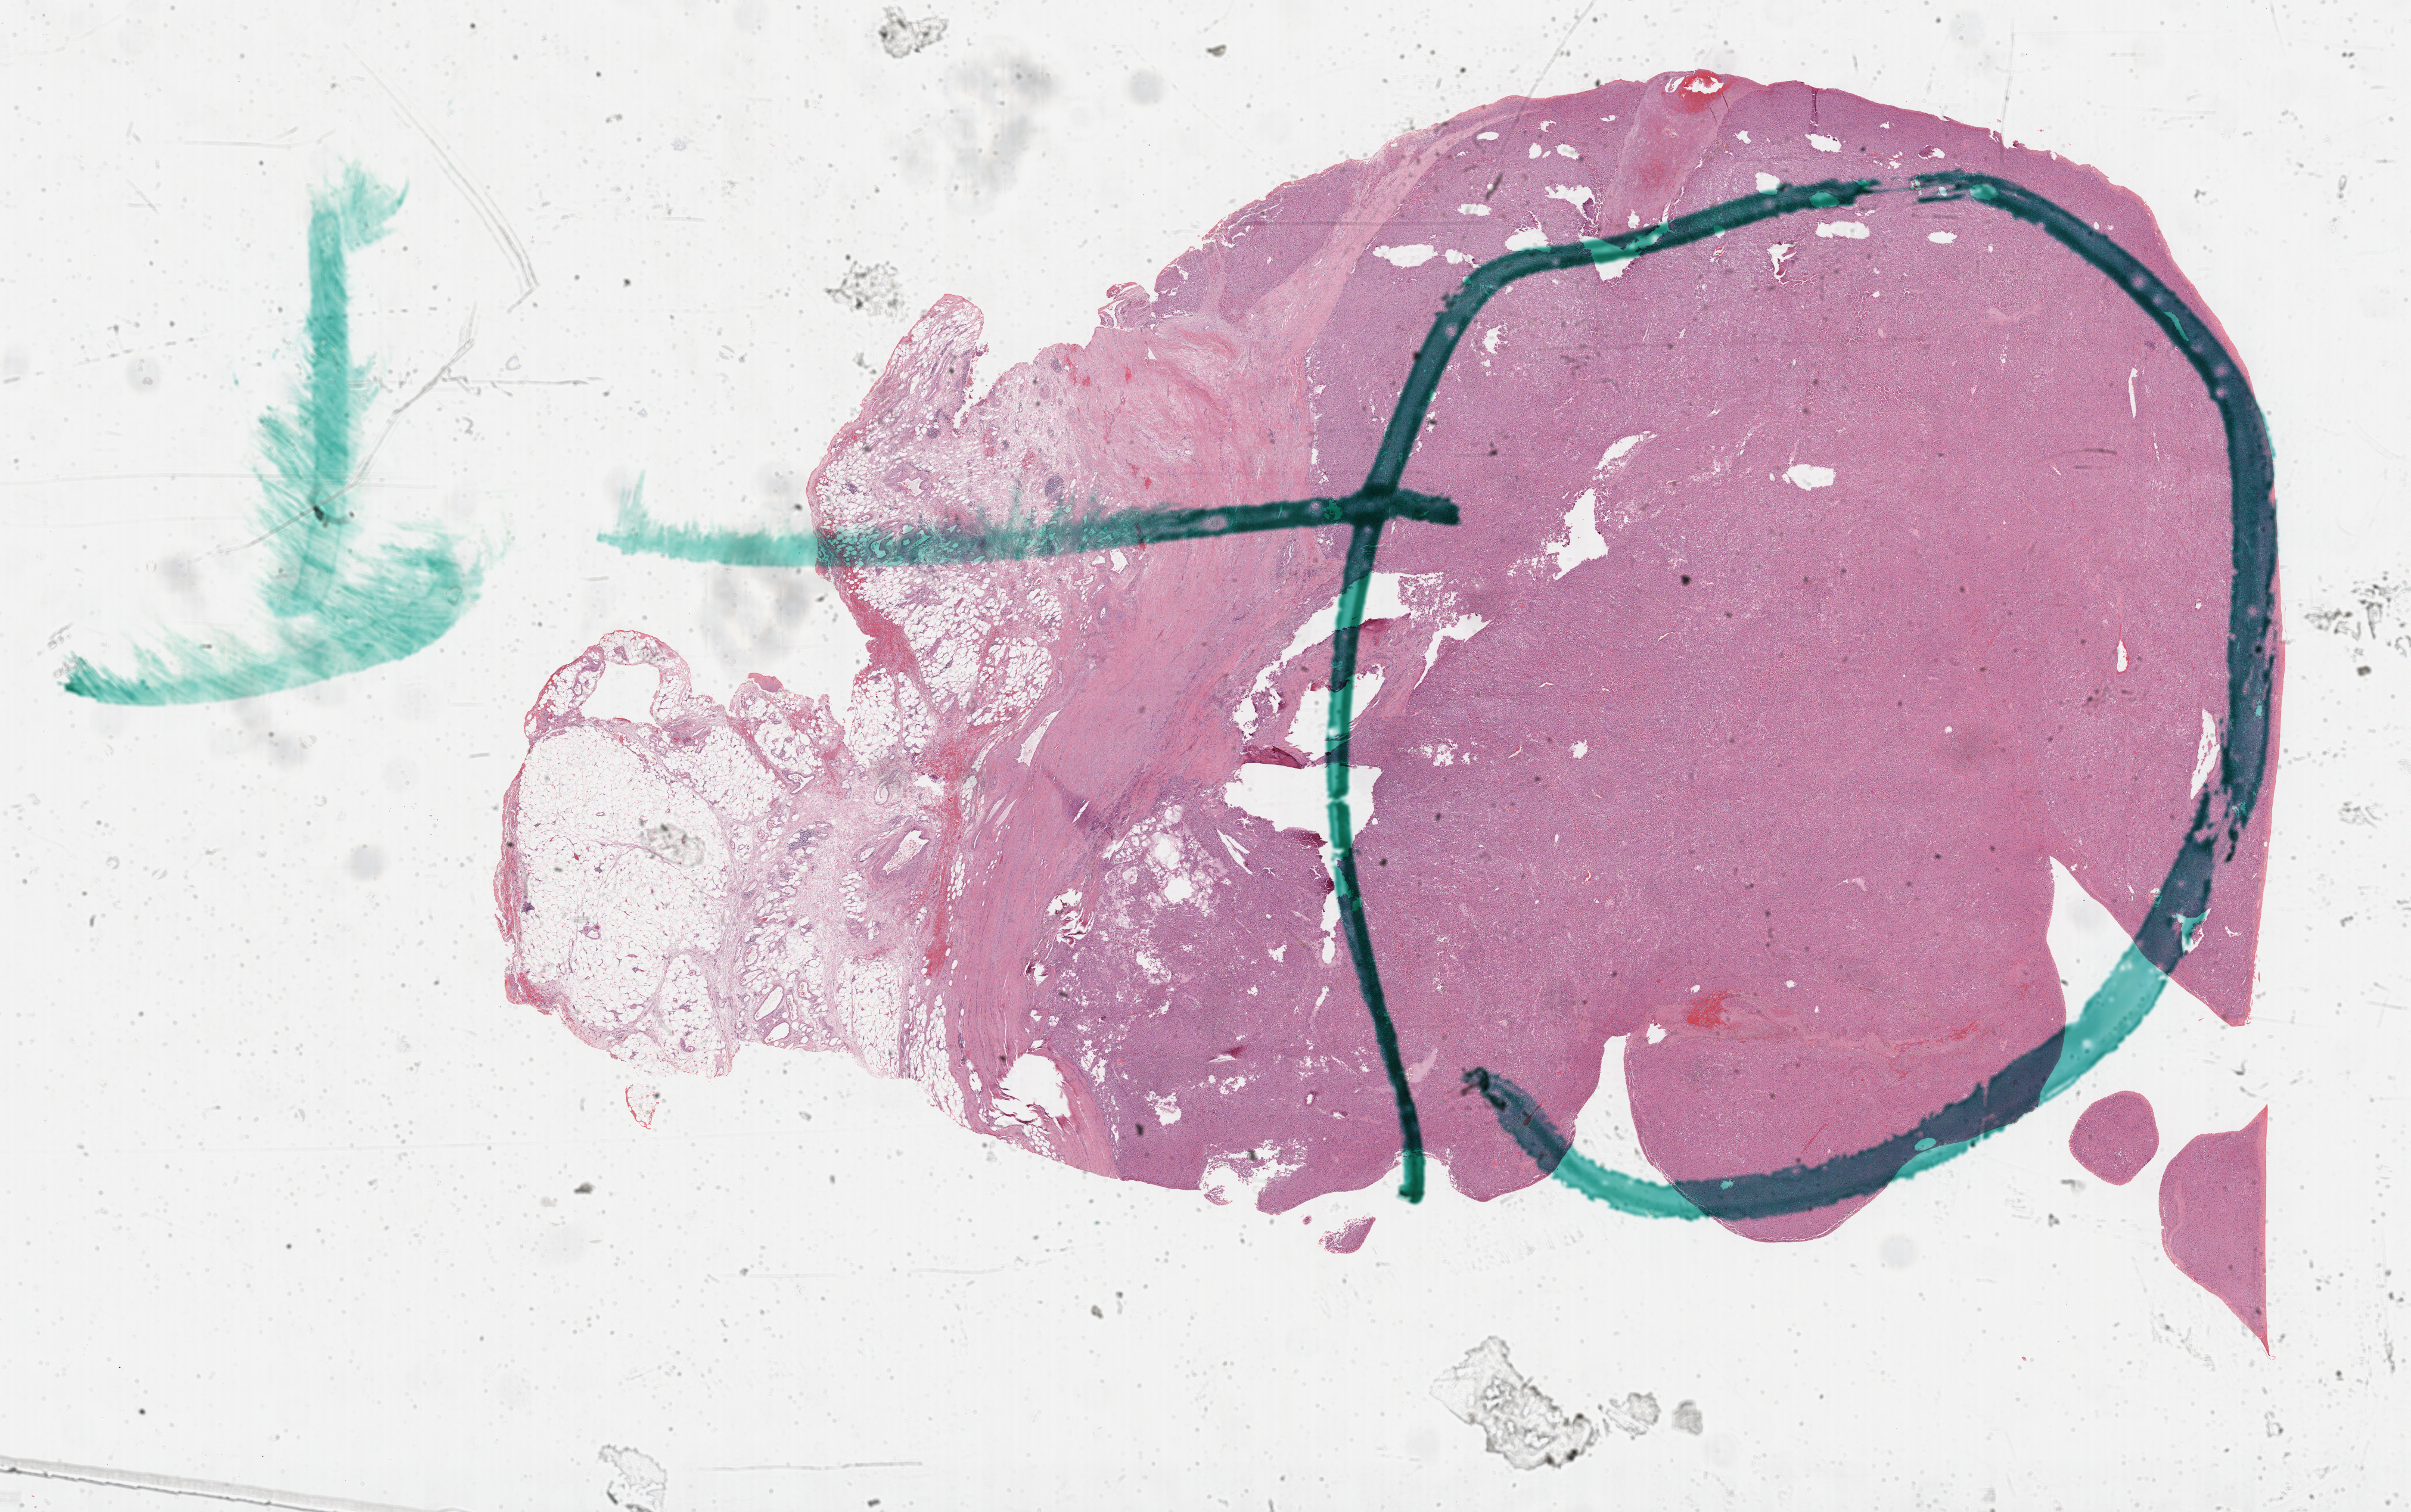
Whole-slide histology image, H&E-stained, a low-resolution overview of the entire scanned area, about 32.7 x 20.5 mm (acquisition: 40x scan), formalin-fixed paraffin-embedded (FFPE) diagnostic section, sample: primary tumour, adrenal cortex. Male, age 53 years at initial diagnosis.
Diagnosis: Adrenal cortical carcinoma (cortex of adrenal gland). Laterality: left.